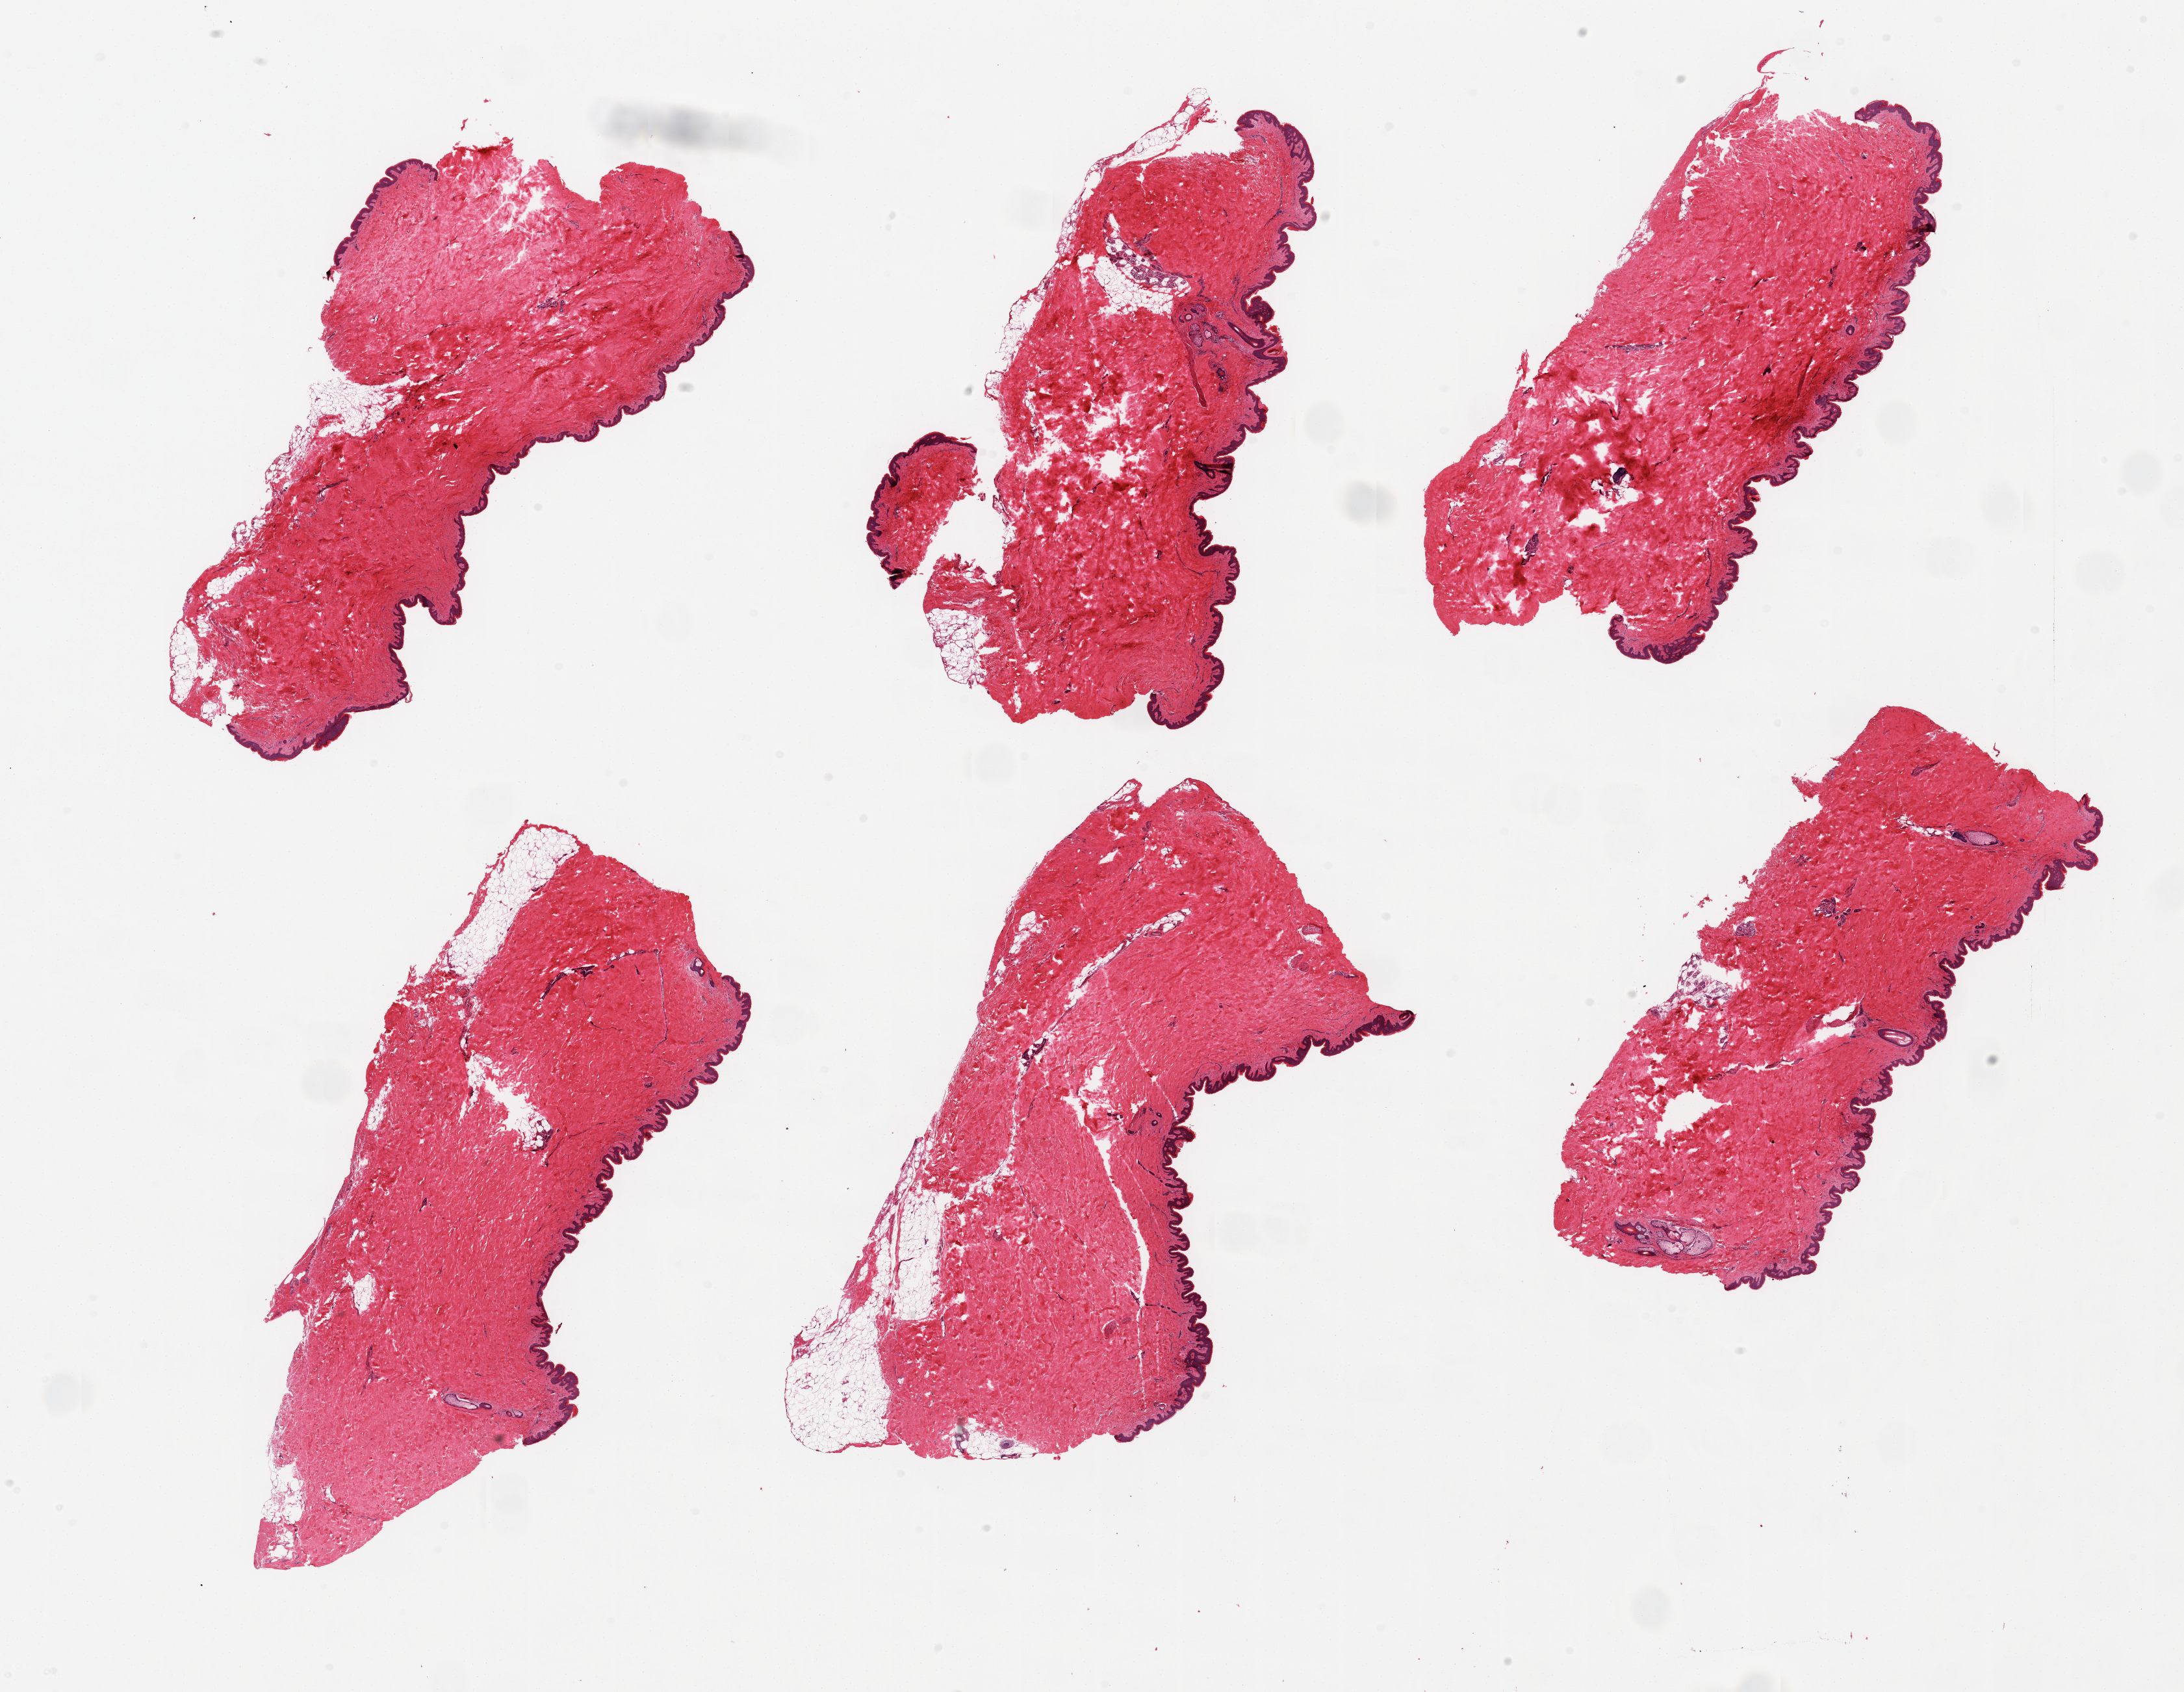
Digitized hematoxylin and eosin (H&E)-stained section, brightfield, shown as a low-resolution overview of the whole scanned area (about 26.6 x 20.6 mm); PAXgene-fixed, paraffin-embedded tissue; sampled site (target tissue): skin of suprapubic region; tissue donor sample.
Pathologist's review note for this sample: 6 pieces; well trimmed; <5% dermal fat.